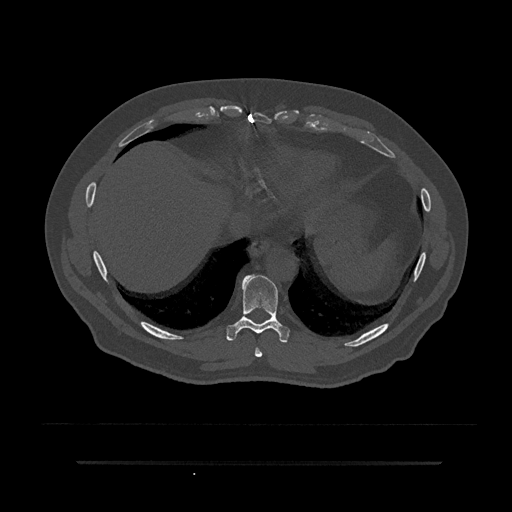
CT including the spine, one axial slice; slice 378 of 797 in the series (ordered by position); bone window (W 1800 / L 400 HU); 512 × 512 image matrix, field of view 464 × 464 mm. Patient: male, 59 years. Case-level facts recorded for this patient, not image findings: primary cancer: bile ducts; vertebrae with lytic lesions (as recorded): T10.
Annotated regions visible in this slice (semi-automatic segmentation, software-assisted and operator-edited):
- T8 vertebra: bounding box [x1, y1, x2, y2] px = [255, 347, 263, 357]
- T9 vertebra: [226, 274, 290, 343]